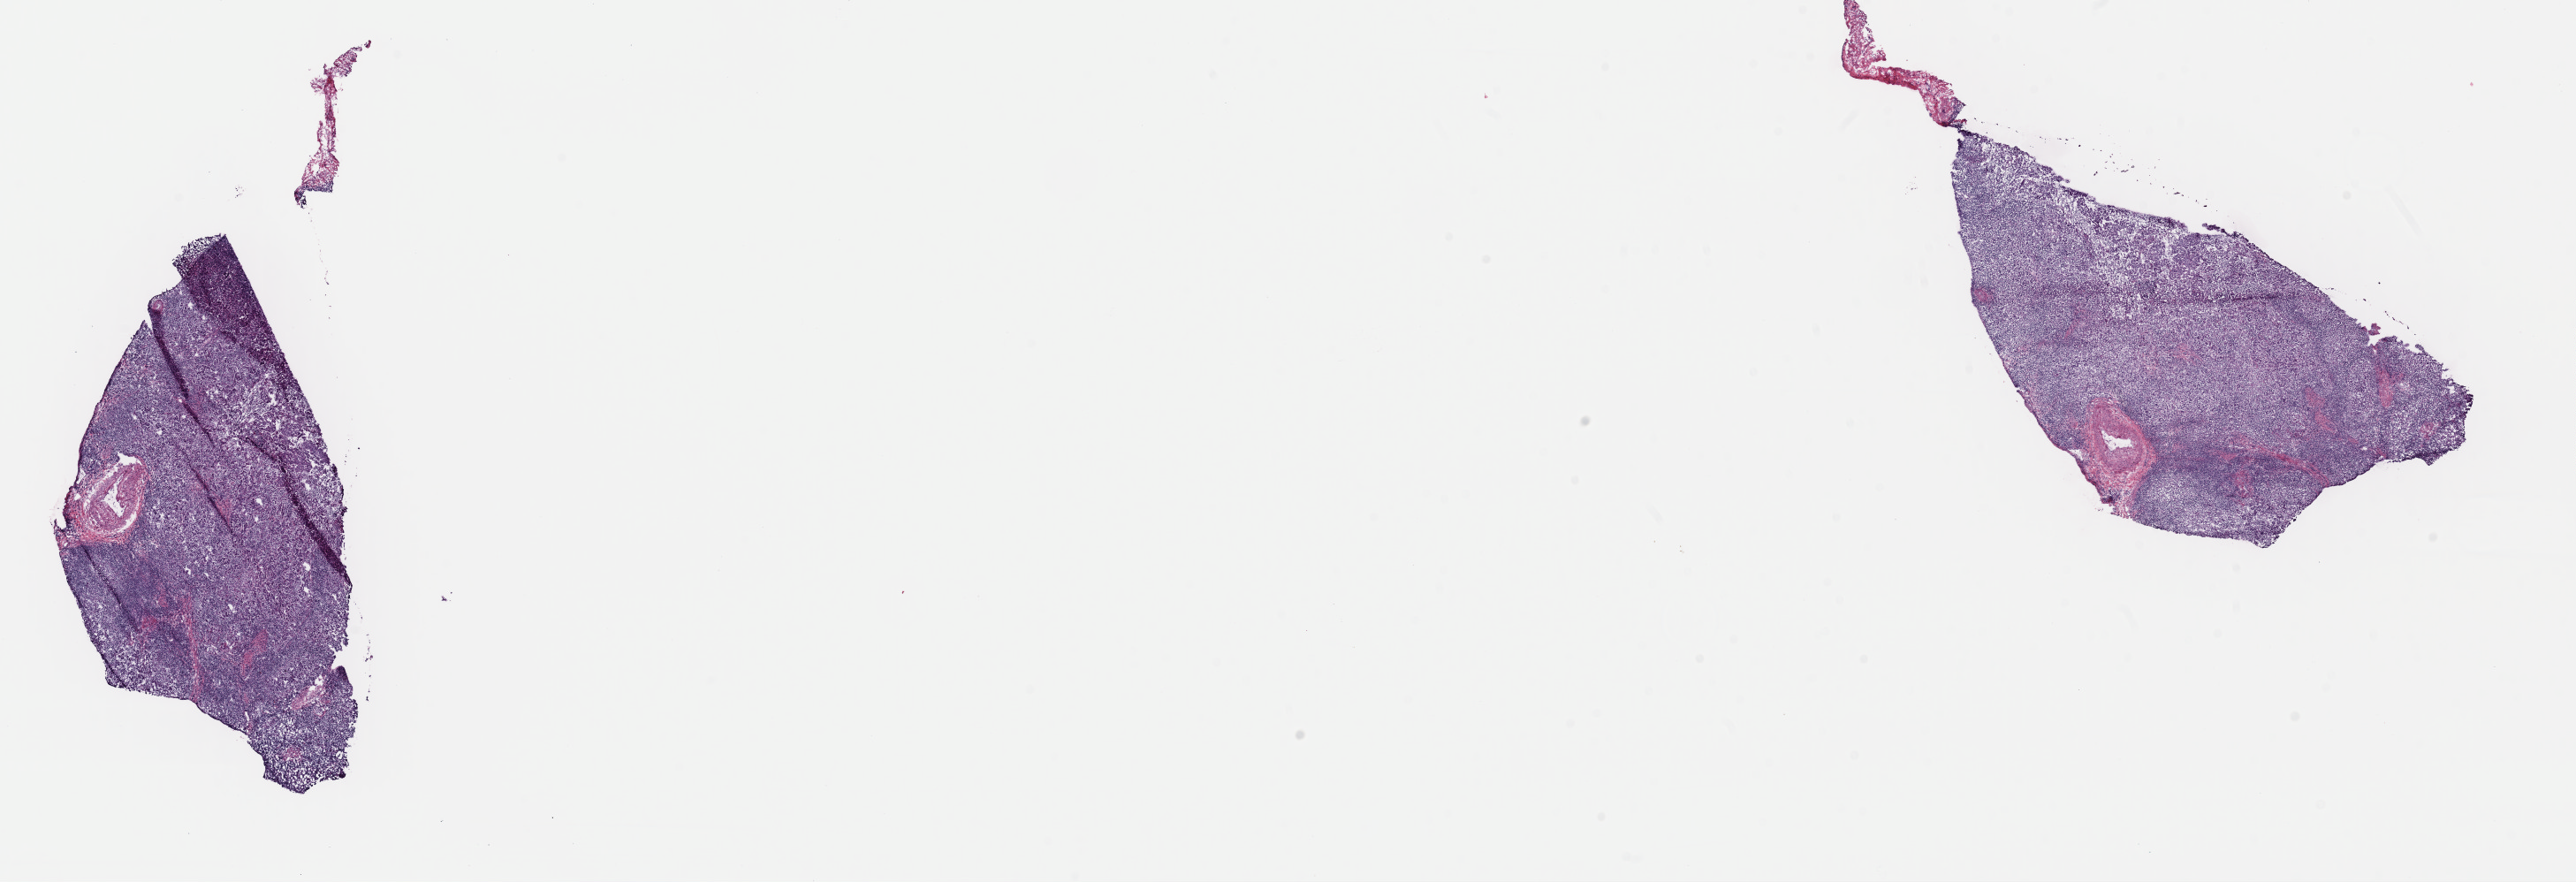
Whole-slide histology image, Hematoxylin and eosin (H&E) stained — whole scanned area (about 23.0 x 7.9 mm, from a 40x scan) shown as a low-resolution overview. Frozen section from the top of the tissue portion. Primary tumour sample from the cervix. Female patient; age at initial diagnosis 46 years. Histologic grade: G2 (moderately differentiated). Pathologist review of this section (percent, as recorded): tumour cells 90%, tumour nuclei 90%, normal cells 0%, stromal cells 10%, necrosis 0%. Inflammatory infiltration, as recorded: lymphocyte infiltration 60%, monocyte infiltration 10%, neutrophil infiltration 10%.
* FIGO stage: IB1
* pathologic diagnosis: Squamous cell carcinoma, NOS